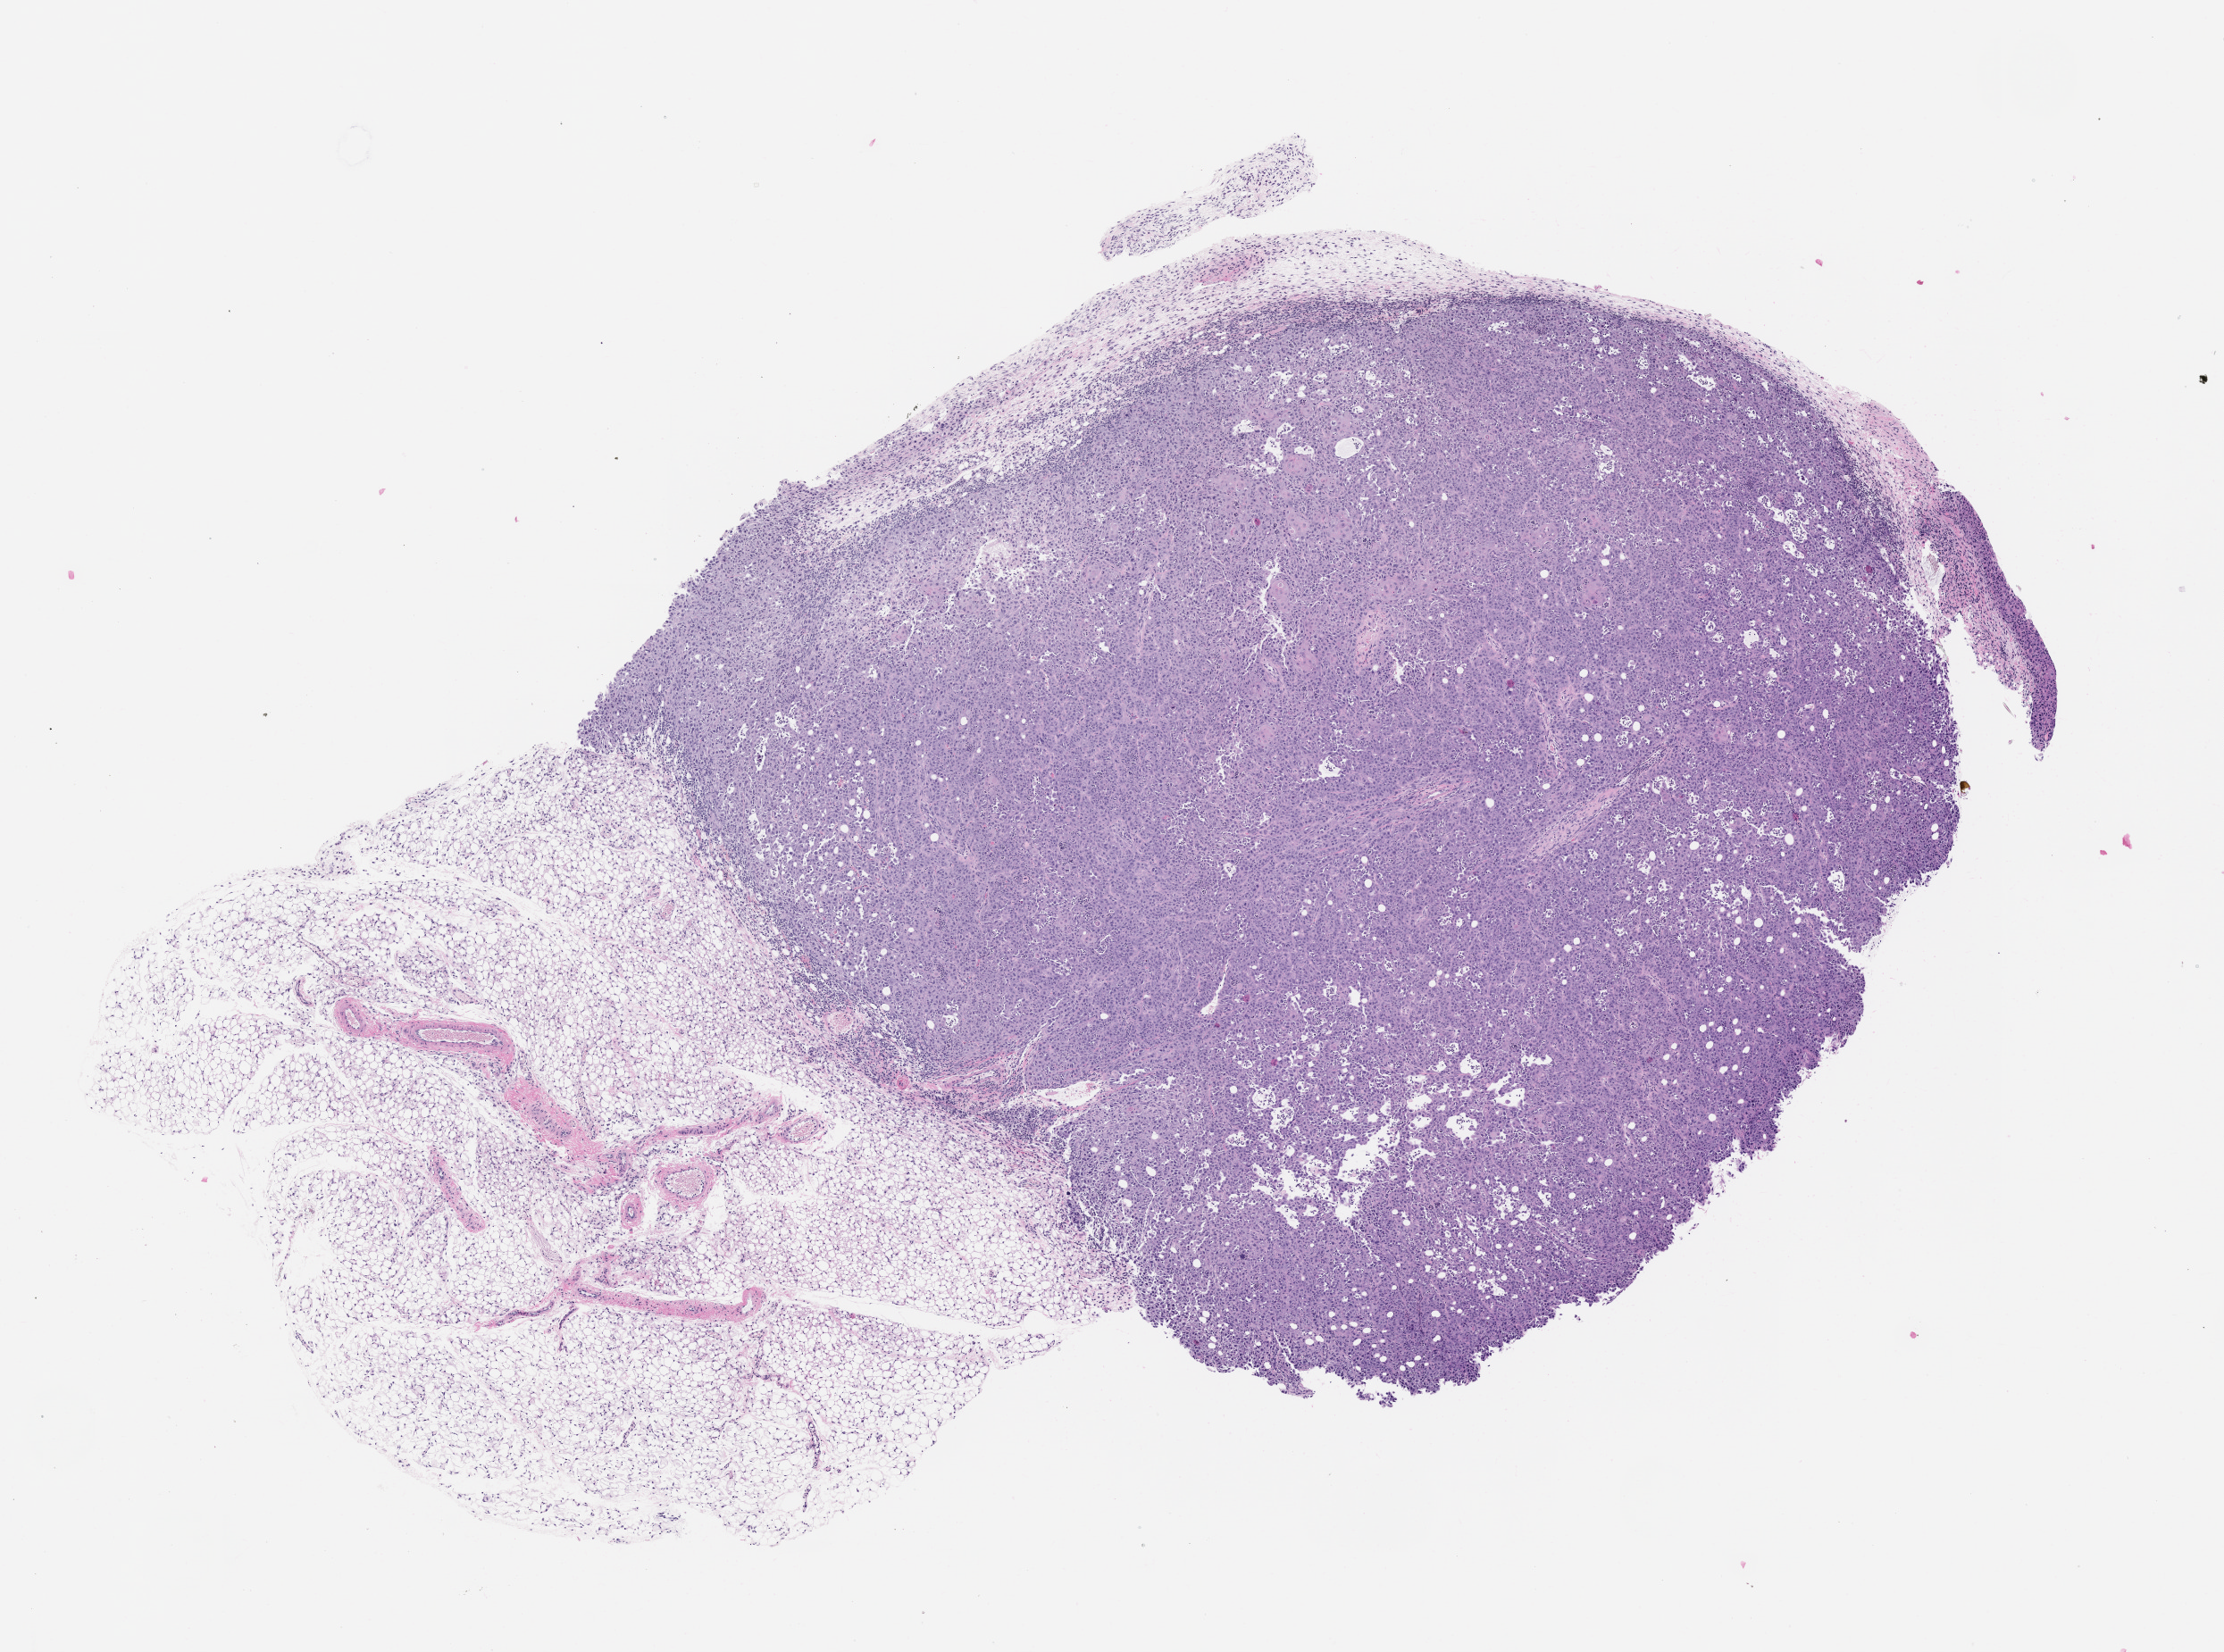
Haematoxylin and eosin whole-slide image of a patient-derived xenograft (PDX) tumor grown in a mouse, passage 3 — shown as a low-resolution overview of the whole scanned area (about 10.0 x 7.4 mm); FFPE section; originating tumor site category: oral soft tissue.
Originating patient diagnosis: Head and Neck Squamous Cell Carcinoma.